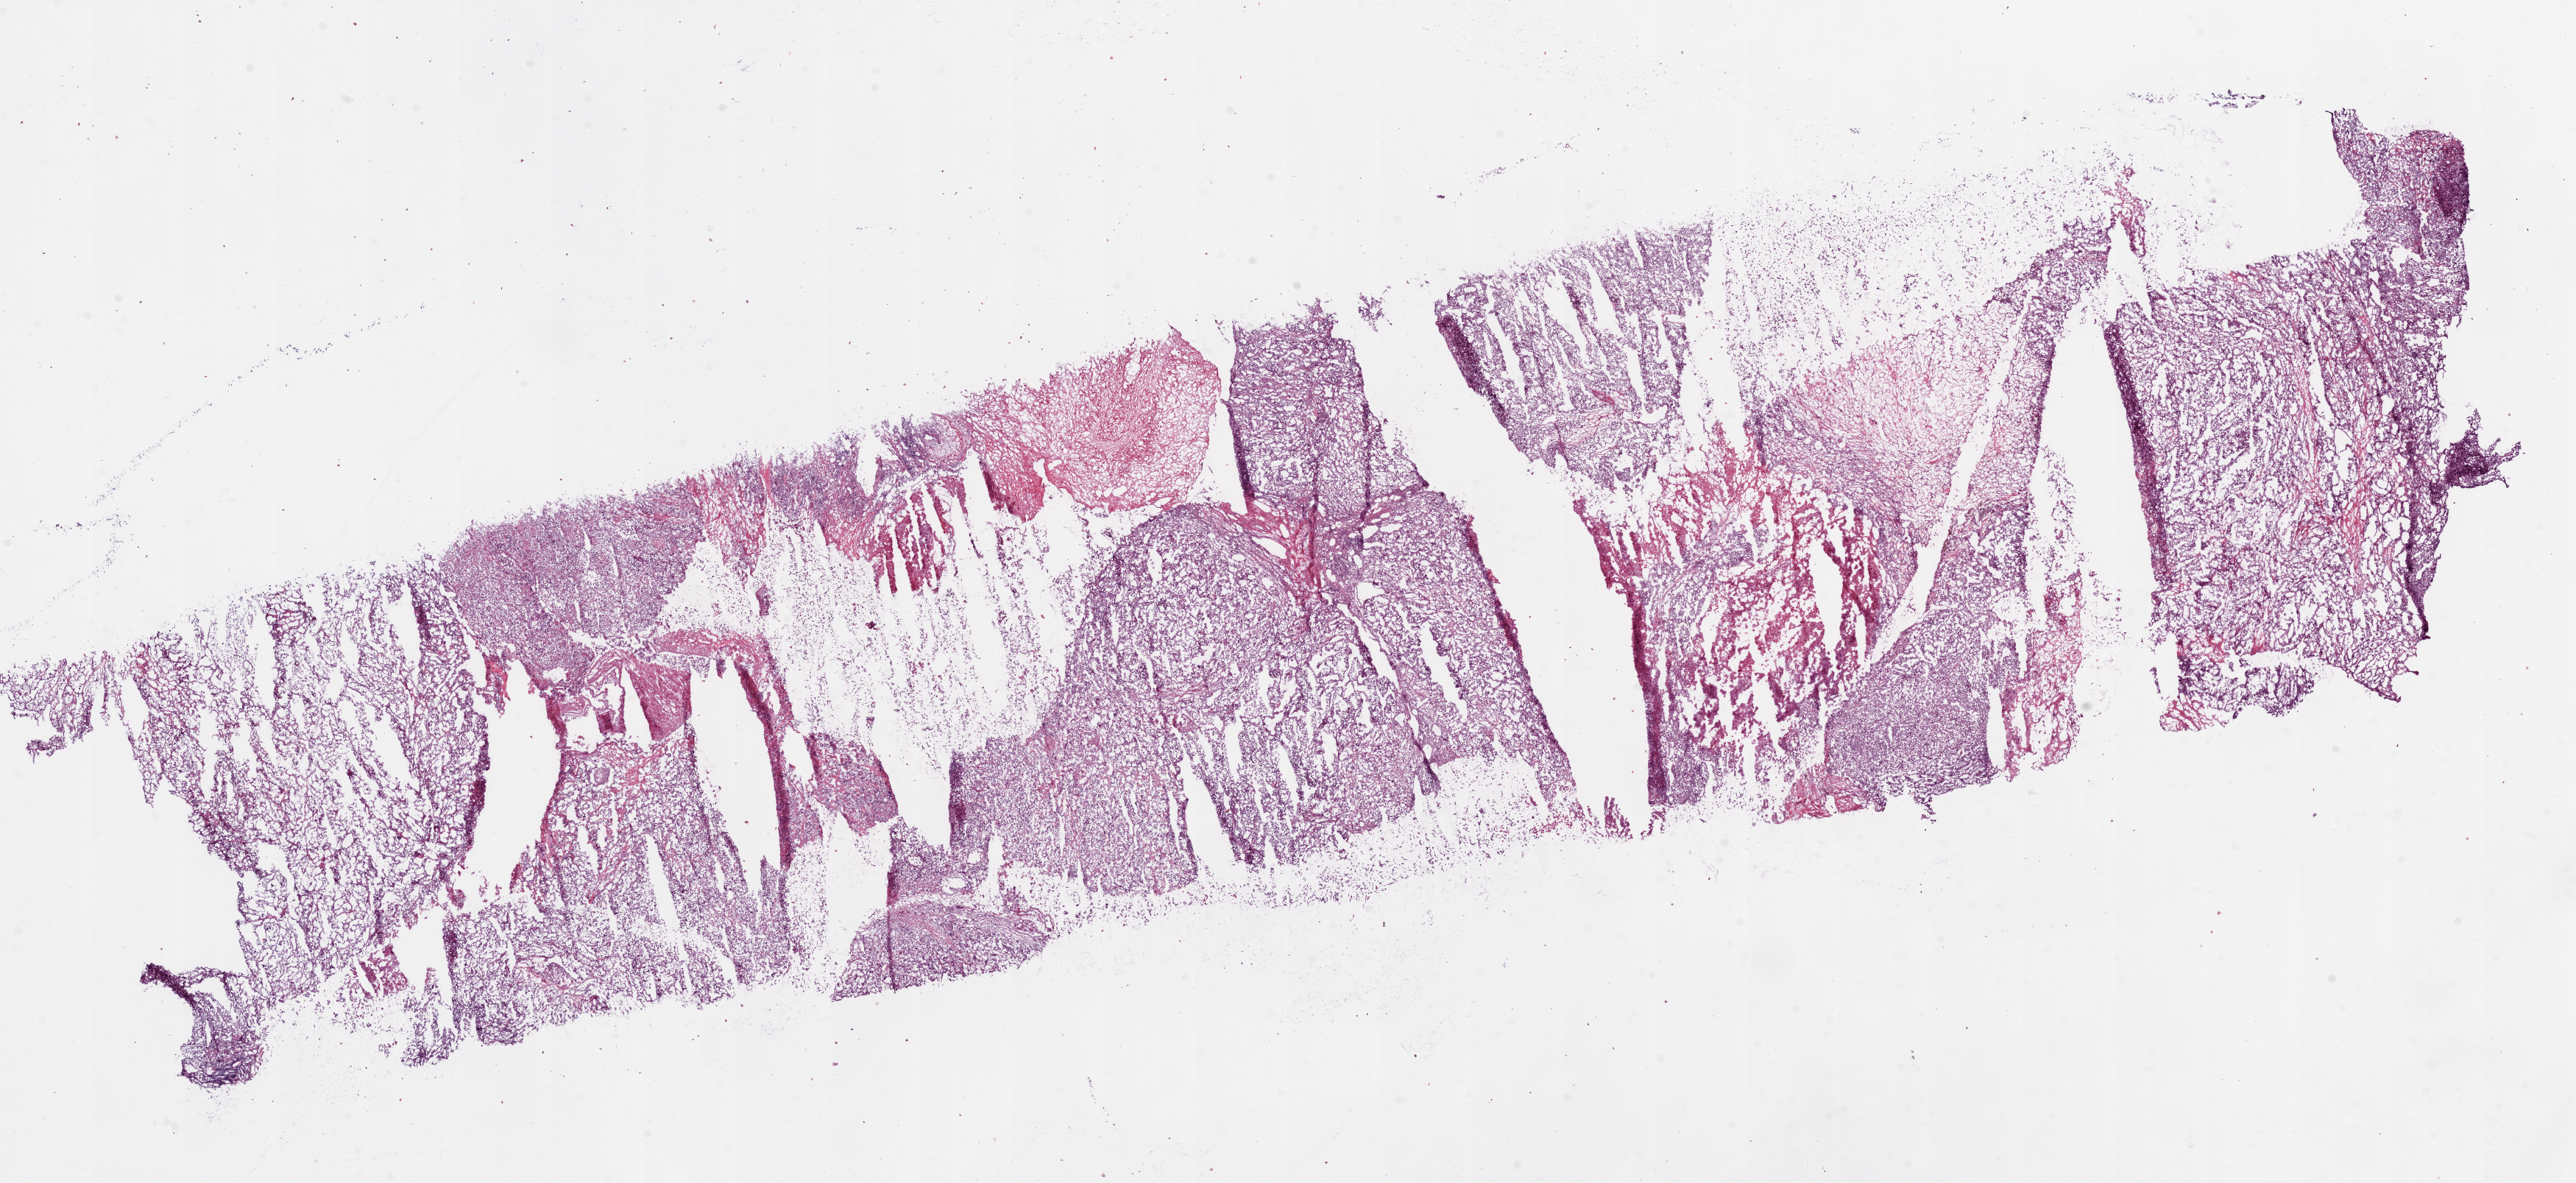
Whole-slide histology image, H&E — low-resolution overview of the scanned area, about 28.1 x 12.9 mm (slide scanned at 20x), frozen section from the bottom of the tissue portion, kidney, primary tumour sample. Female patient; age at initial diagnosis 63 years. Histologic grade: G4 (undifferentiated). Slide review estimates, as recorded: tumour cells 75%, tumour nuclei 85%, normal cells 0%, stromal cells 10%, necrosis 15%.
- TNM: T3a NX M1
- diagnosis: Clear cell adenocarcinoma, NOS
- AJCC pathologic stage: IV